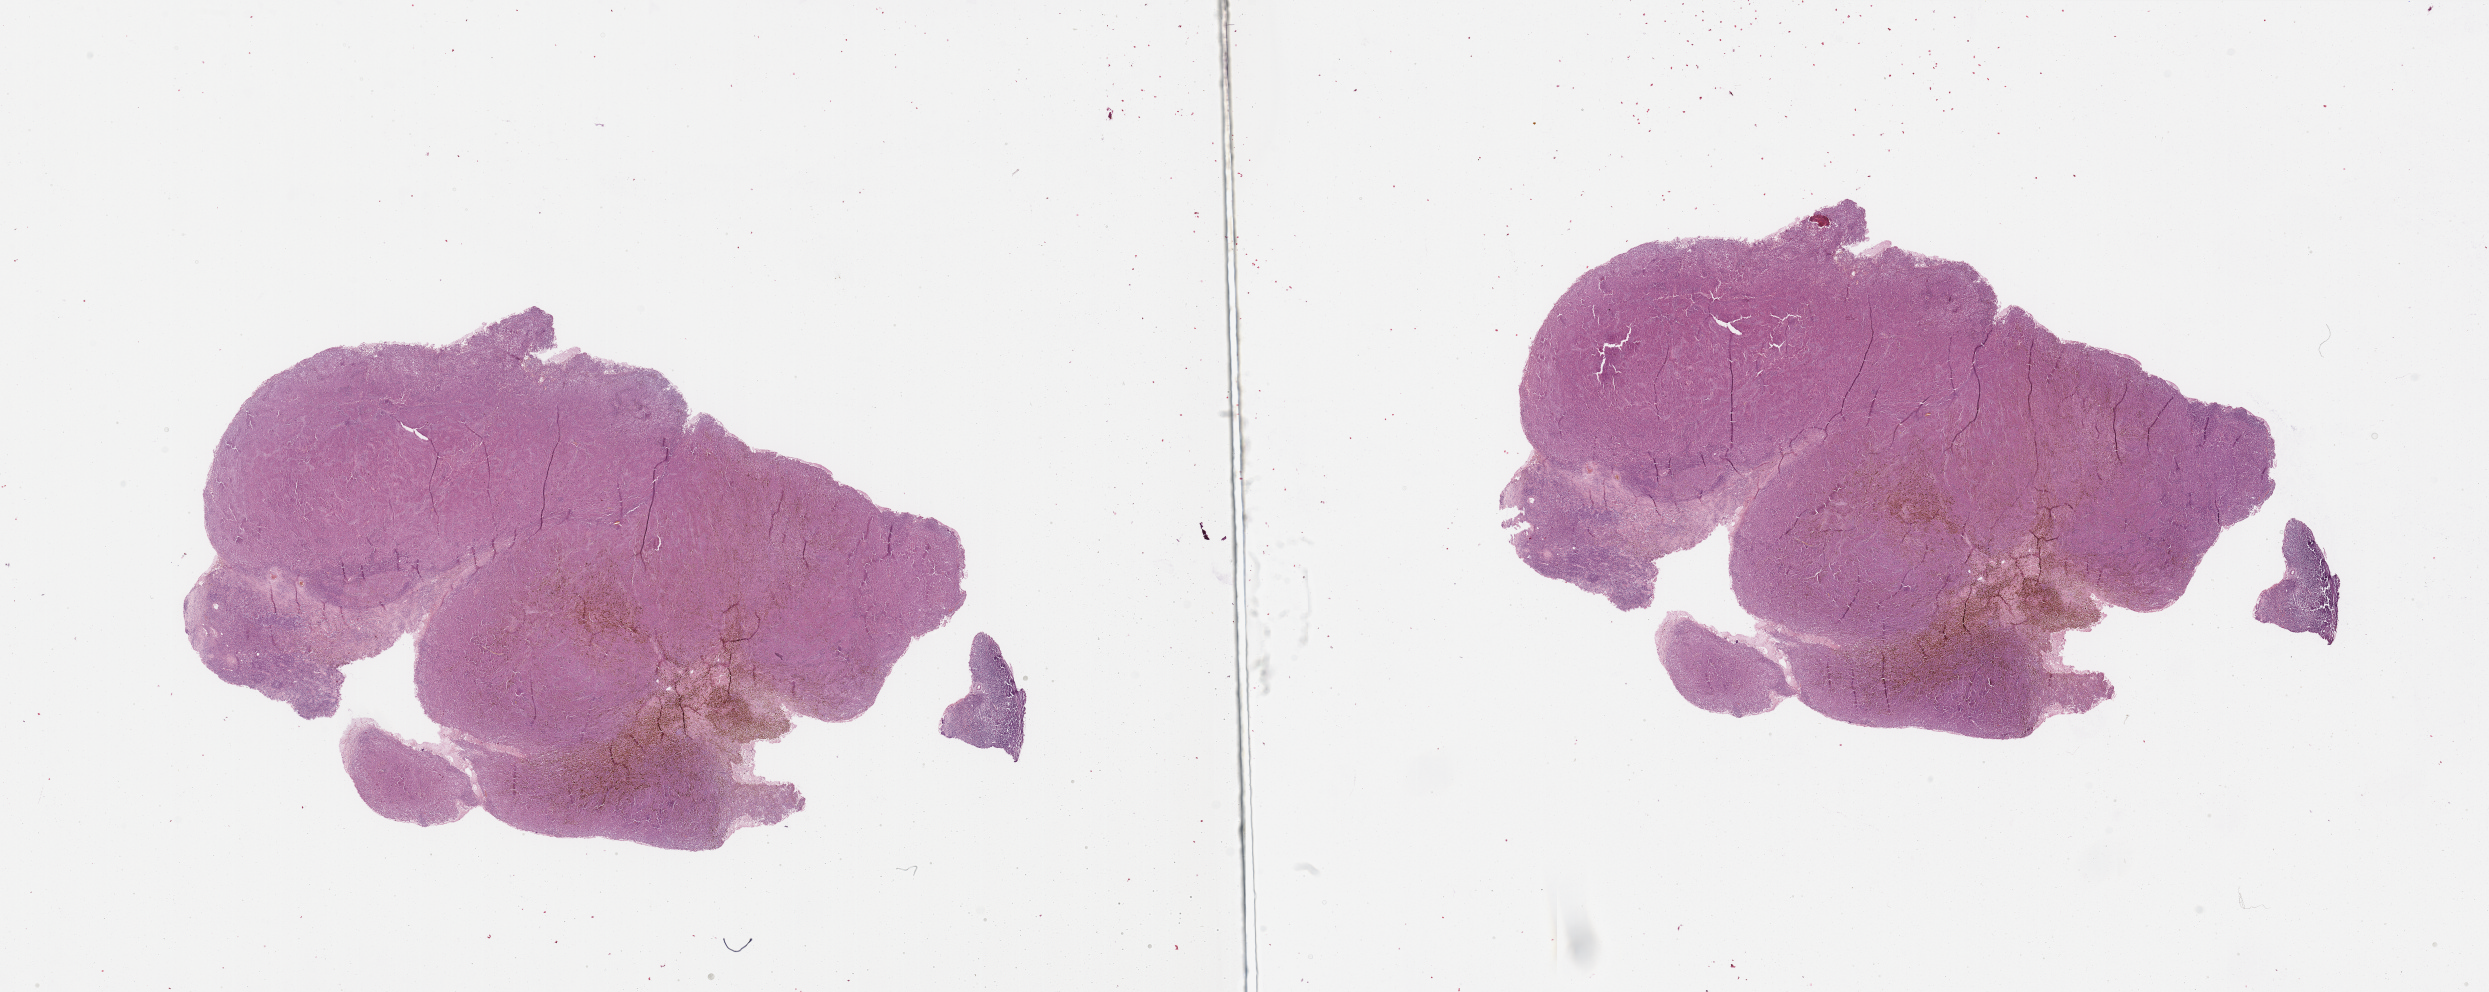
Whole-slide histology image, Hematoxylin and eosin (H&E) stained — shown as a low-resolution overview of the whole scanned area (about 39.4 x 15.7 mm, slide scanned at 20x). Tumour tissue sample, sampled site: lymph node. 62-year-old male patient. Composition of this section per pathologist review: tumour nuclei 90%, necrosis 3%.
This section: metastatic tumour tissue. Primary tumour site (as recorded): trunk. Patient diagnosis: Malignant melanoma, NOS.